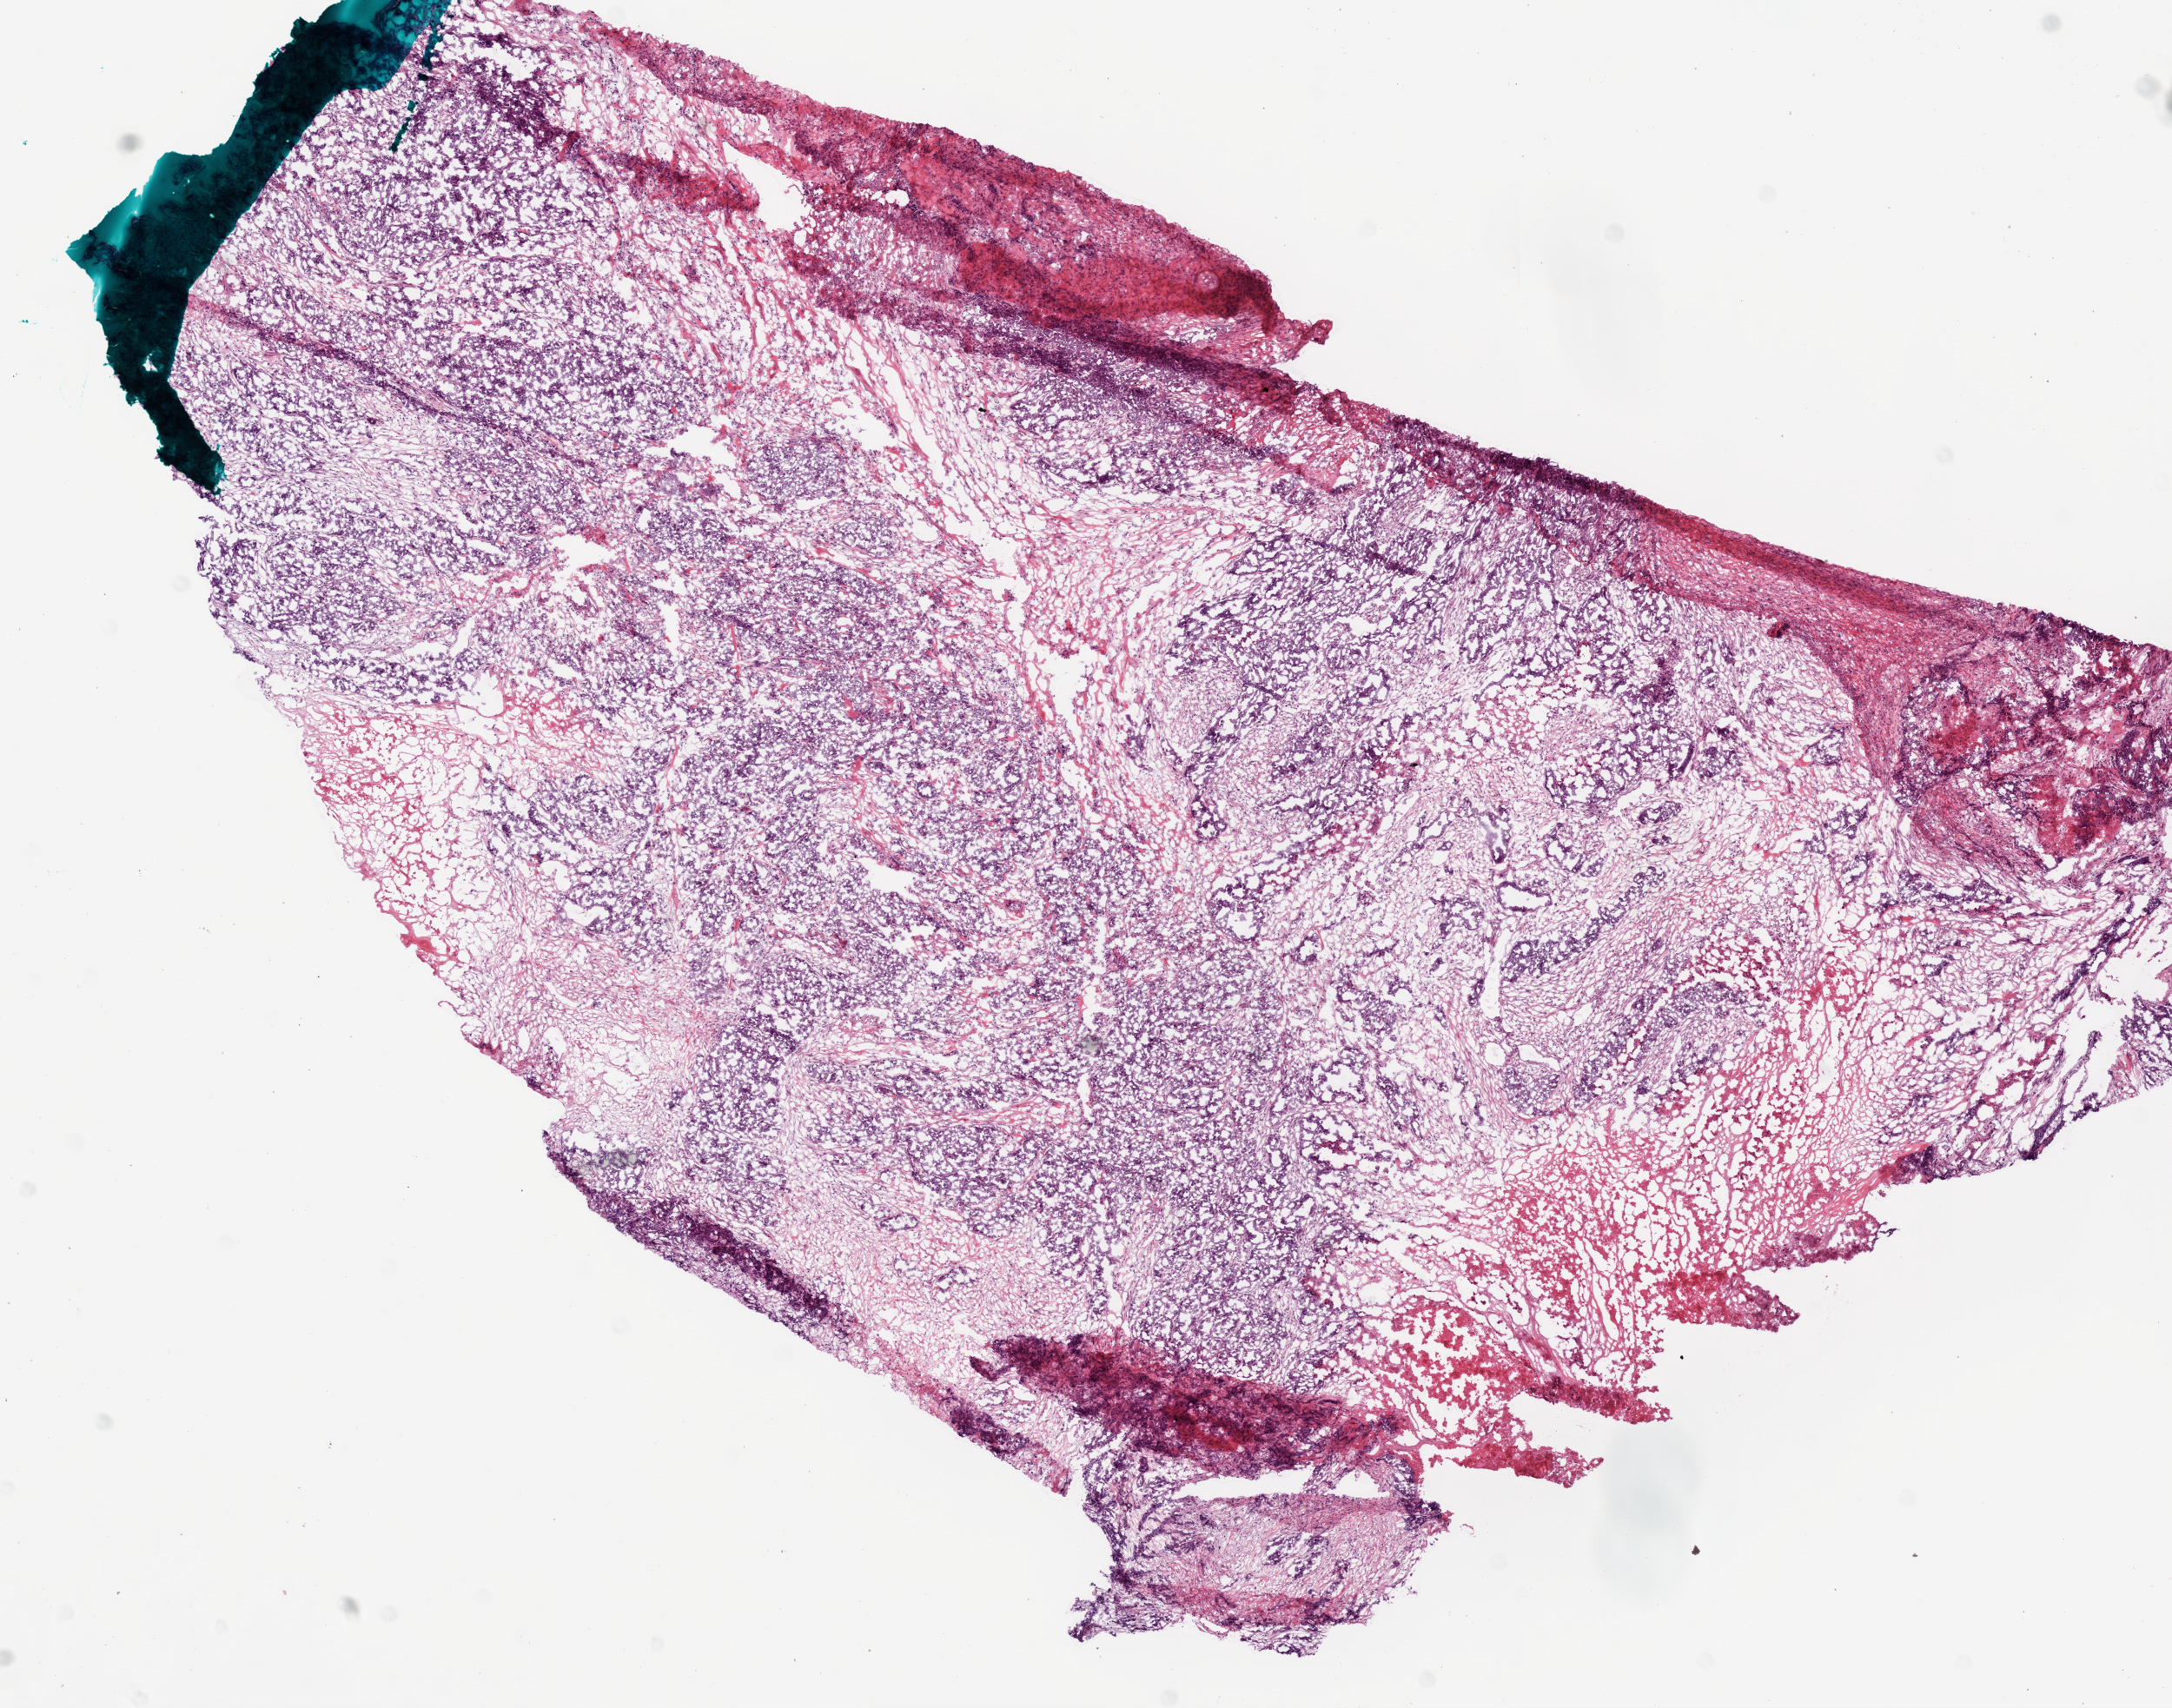
H&E-stained whole-slide image, low-resolution overview of the scanned area, about 10.0 x 7.9 mm (slide scanned at 20x). Frozen section. Primary tumour sample from the ovary. Patient: female, age at initial diagnosis 68 years. Histologic grade: G3 (poorly differentiated). Slide review estimates, as recorded: tumour cells 75%, tumour nuclei 70%, normal cells 15%, stromal cells 0%, necrosis 10%.
• FIGO stage: IIIC
• laterality: bilateral
• diagnosis: Serous cystadenocarcinoma, NOS